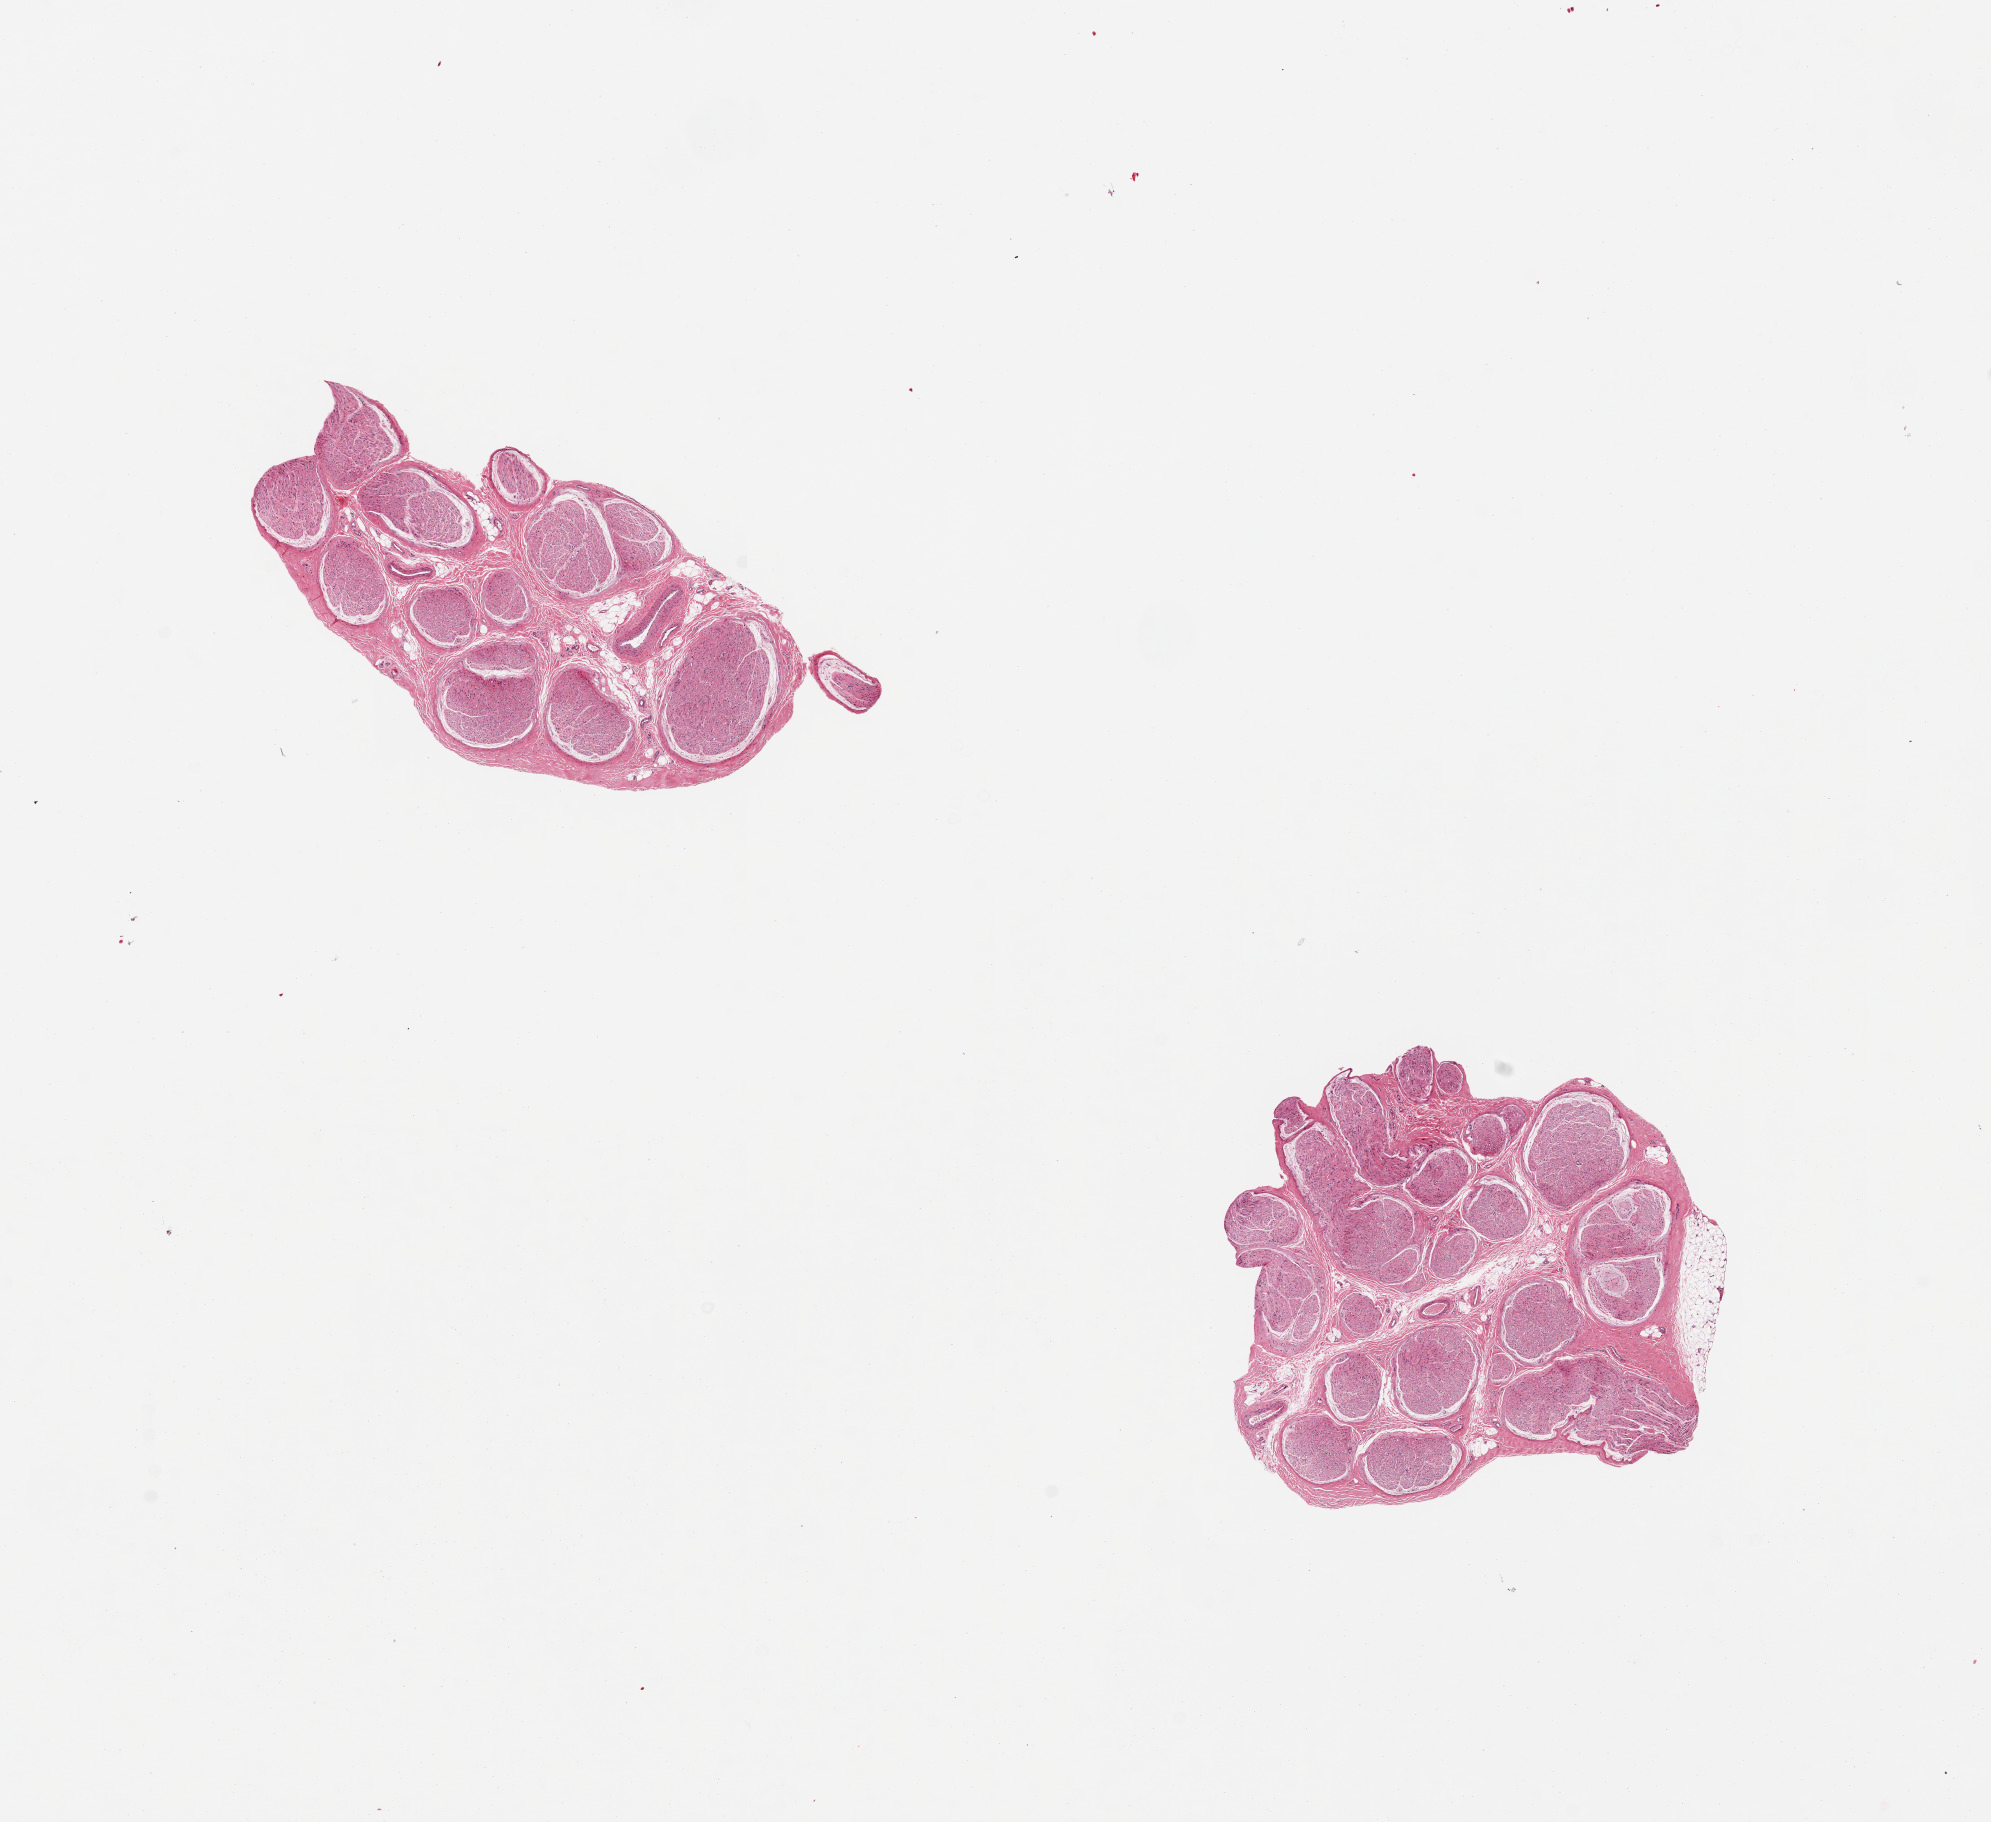
Digitized H&E-stained section — low-resolution overview of the scanned area, about 15.8 x 14.4 mm (acquisition: 20x scan), PAXgene-fixed, paraffin-embedded tissue, target tissue: tibial nerve, tissue donor sample.
• review note (as recorded): 2 pieces, good clean specimens, trace adherent fat